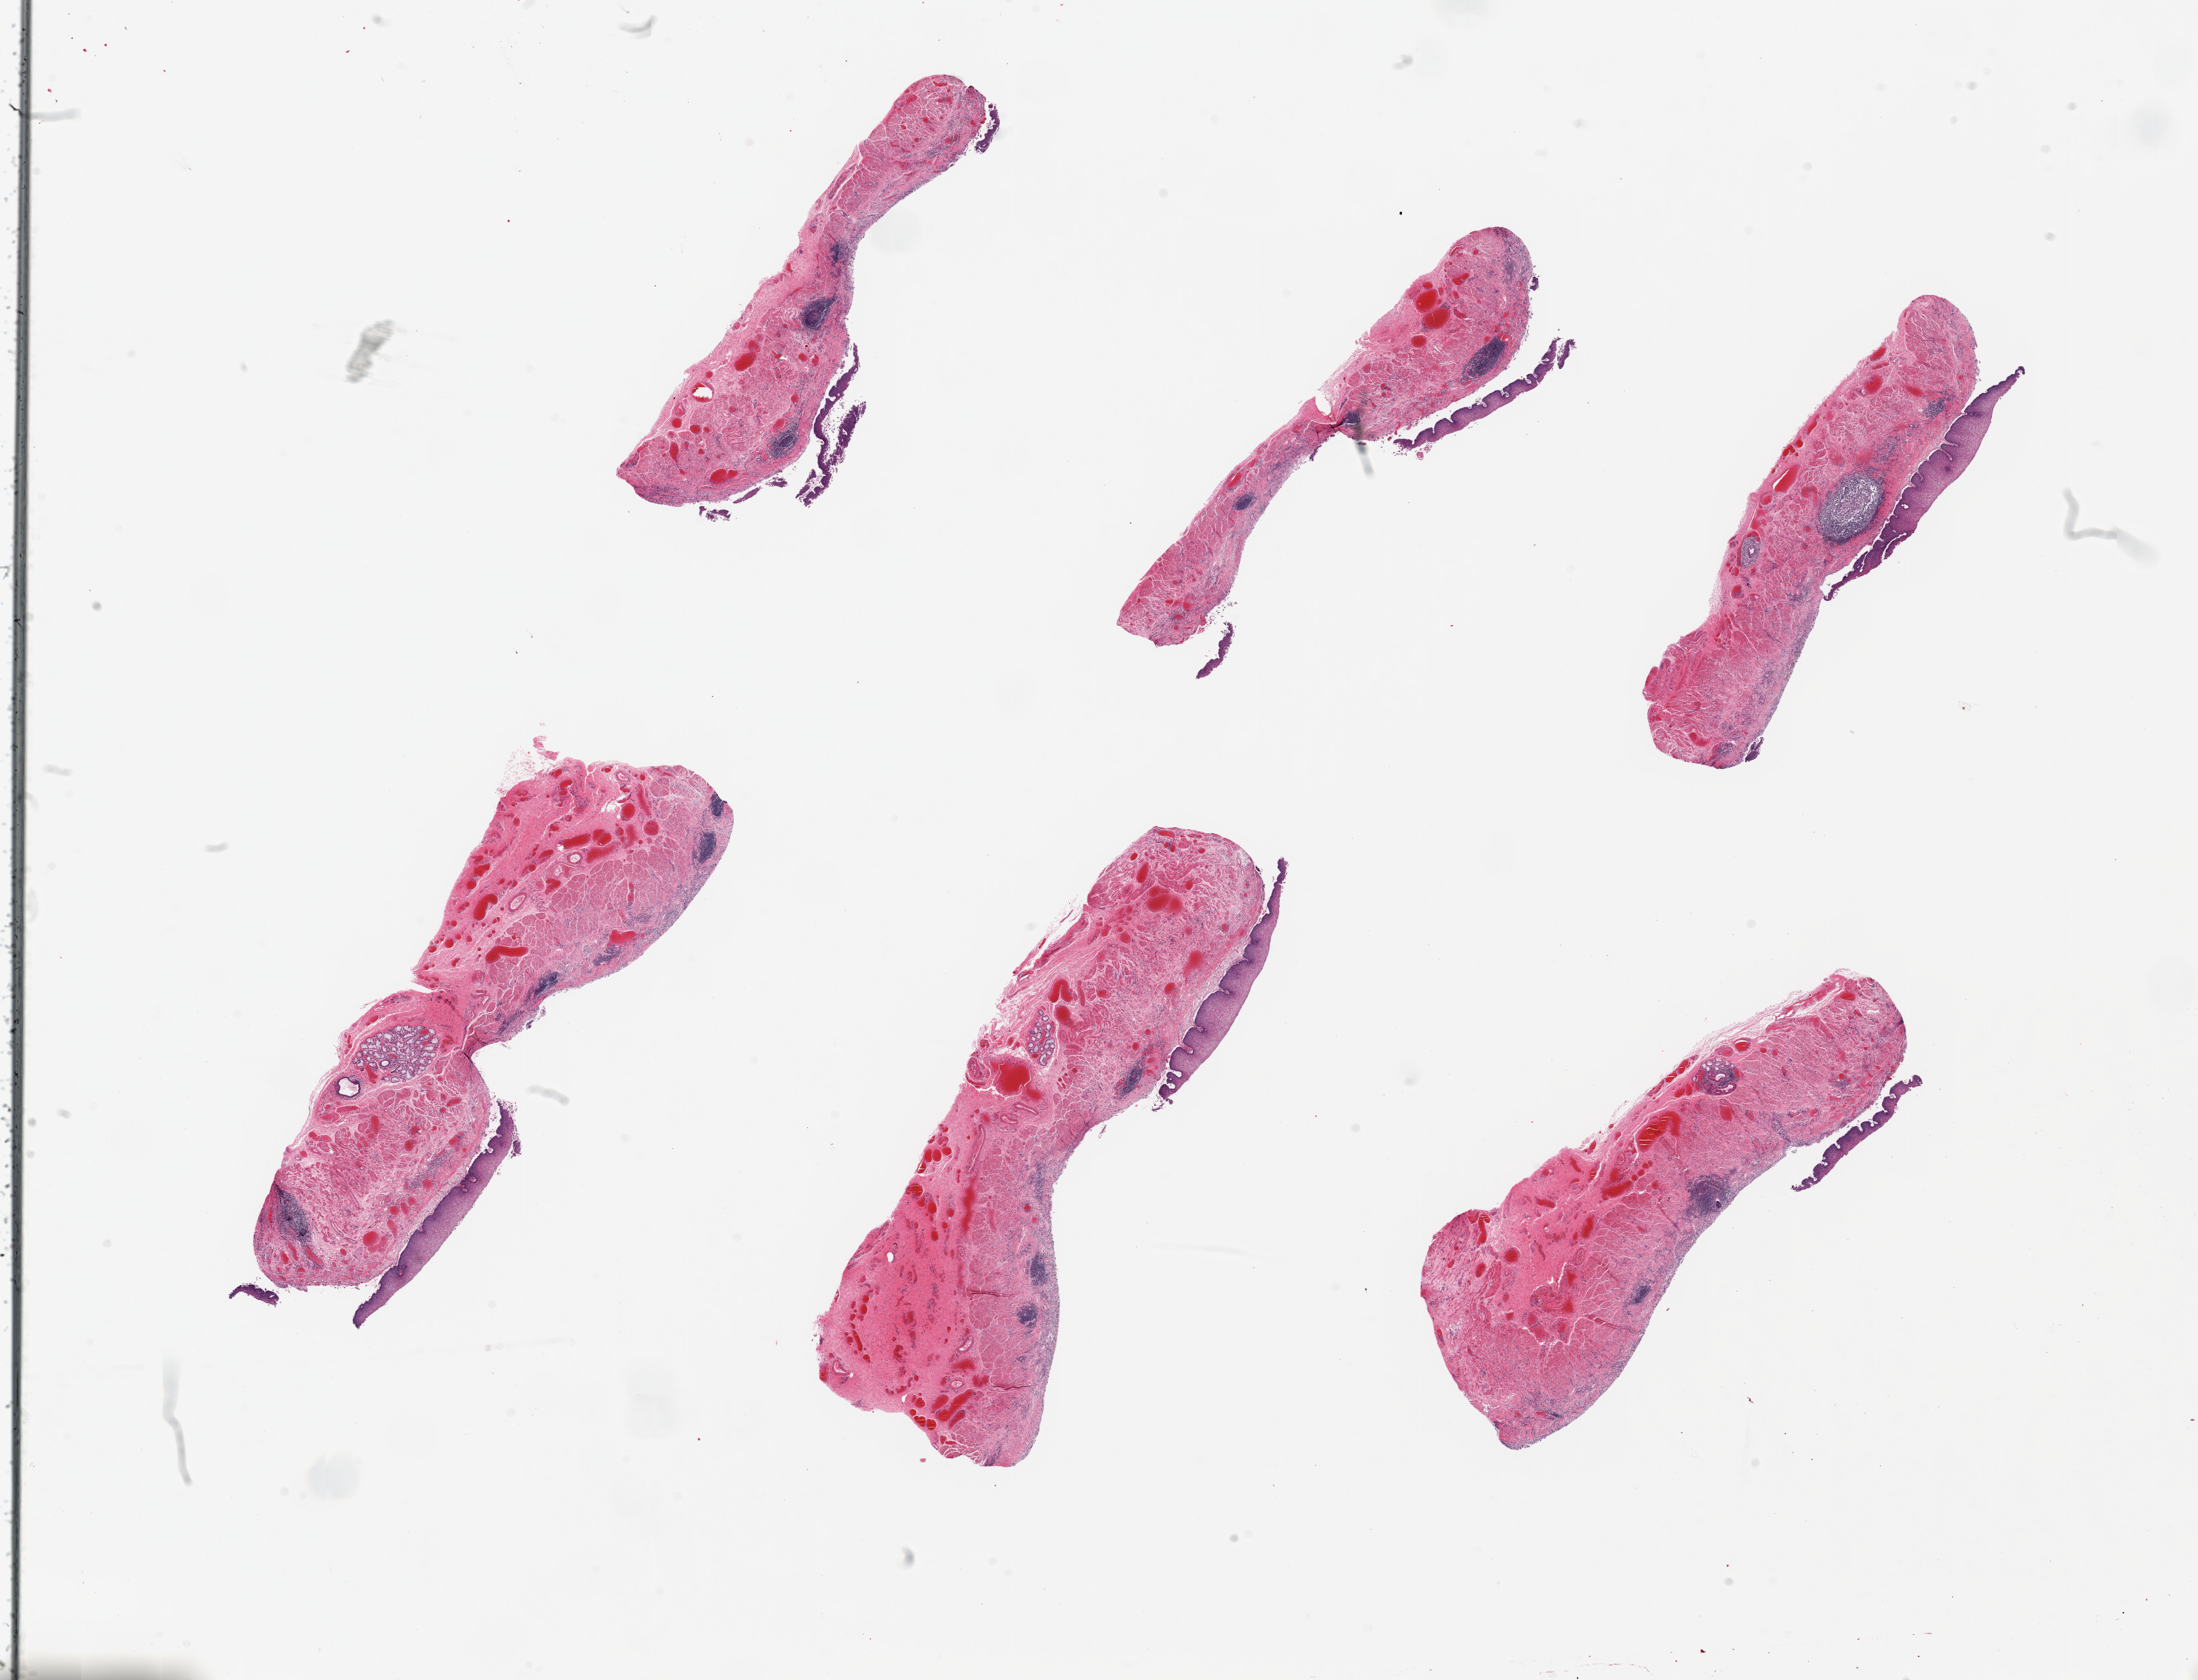
Digitized hematoxylin and eosin (H&E)-stained section, brightfield — shown as a low-resolution overview of the whole scanned area (about 26.6 x 20.3 mm). PAXgene-fixed, paraffin-embedded tissue. Sampled site (target tissue): esophageal mucous membrane. Donor tissue sample. Donor: male.
Review note (as recorded): 6 pieces, up to 8x3mm; squamous mucosa sloughing/denuded, chronic/erosive inflamation present.